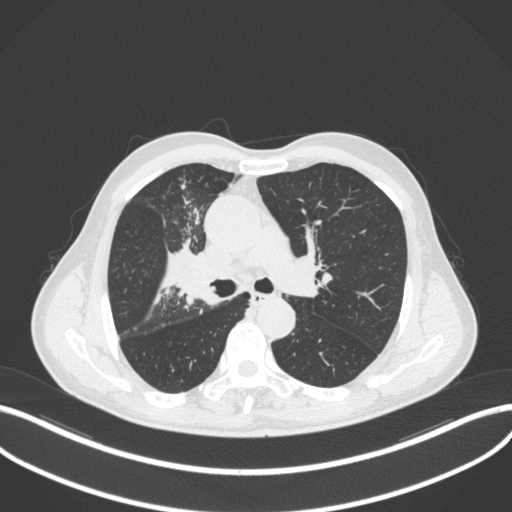
Chest CT, one axial slice. Slice 308 of 490 in the series (ordered by position). Reconstruction kernel B31f. 120 kVp. Lung window (W 1500 / L -600 HU). 1 mm slice thickness. 512 × 512 image matrix, field of view 400 × 400 mm. Patient: male, 69 years. Case-level facts recorded for this patient, not image findings: clinical TNM (as recorded): T2a N0 M0.
Outlined on this slice (bounding box drawn by a radiologist):
- lung tumour (recorded histology: adenocarcinoma): box from (x=173, y=246) to (x=213, y=308) px